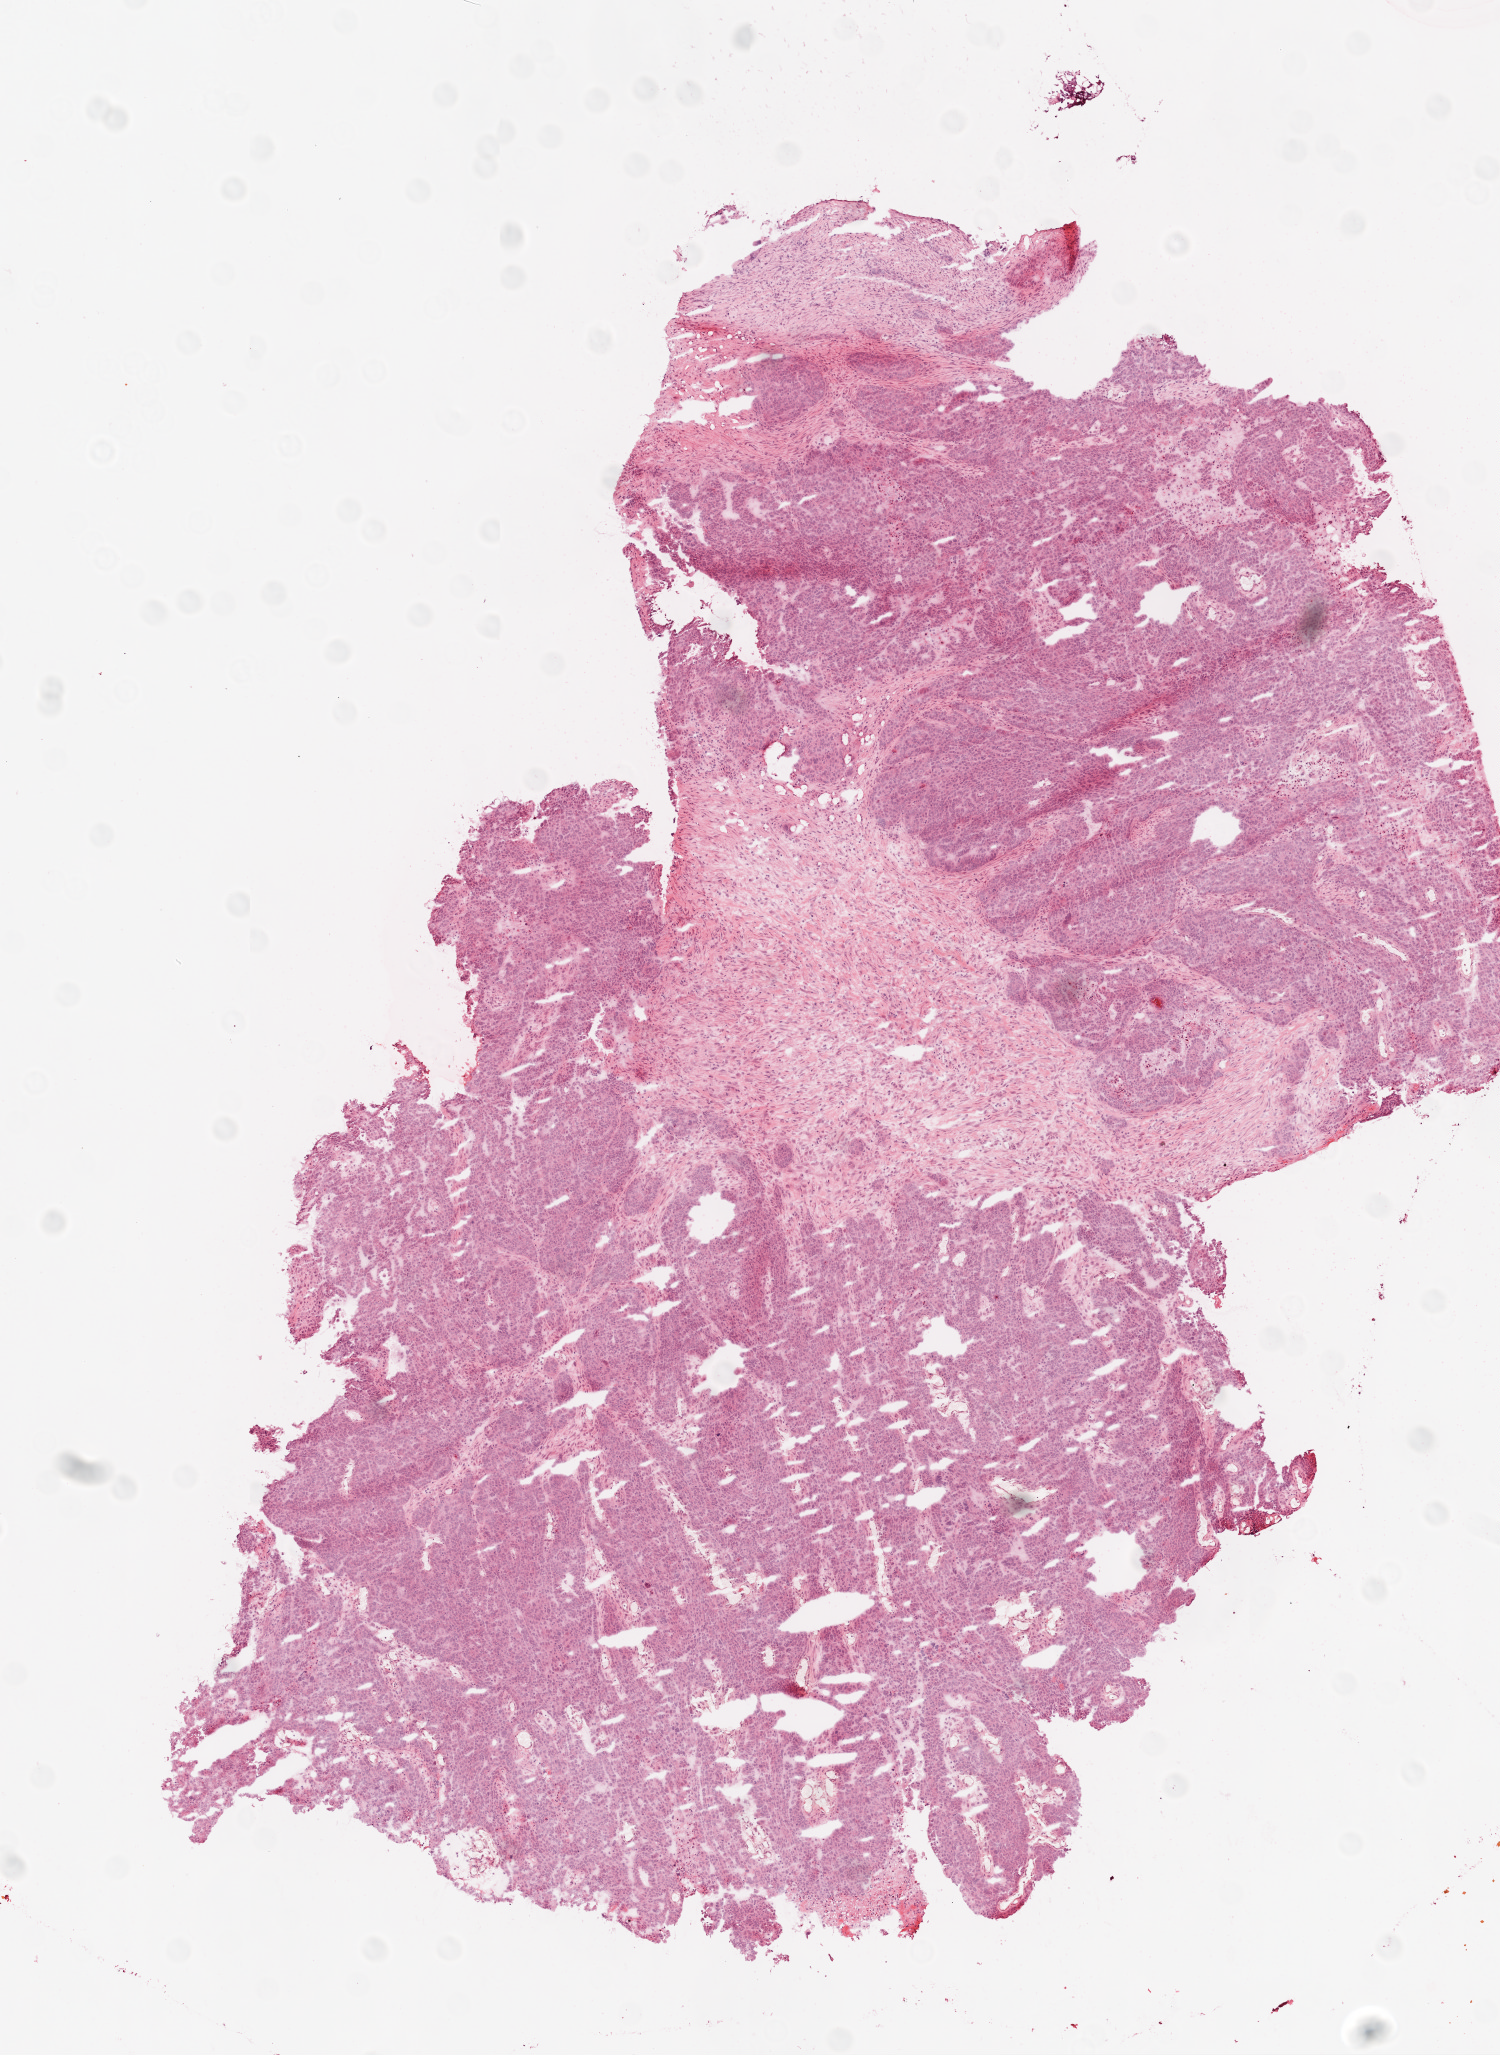
Whole-slide histology image, H&E-stained, a low-resolution overview of the entire scanned area, about 6.0 x 8.2 mm (acquisition: 20x scan). Frozen section. Sample: primary tumour, ovary. Female patient; age at initial diagnosis 58 years. Histologic grade: G3 (poorly differentiated). Composition of this section per pathologist review: tumour cells 80%, tumour nuclei 95%, normal cells 0%, stromal cells 19%, necrosis 1%.
• histologic diagnosis: Serous cystadenocarcinoma, NOS
• FIGO stage: IIIC